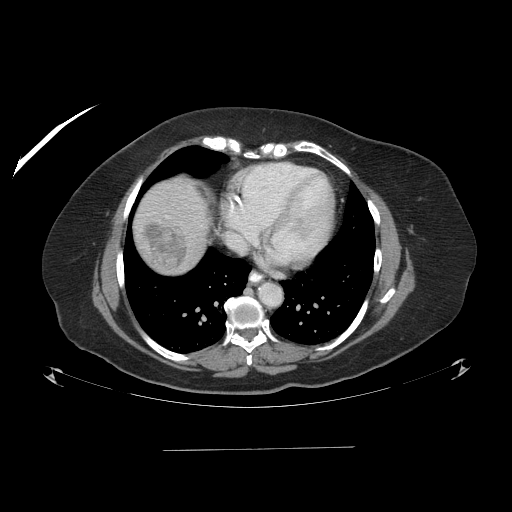
Contrast-enhanced abdominal CT (liver protocol), one axial slice. Slice 83 of 103 in the series (ordered by position). Reconstruction kernel STANDARD. 120 kVp. One of 2 acquisitions stored at this slice position. Soft-tissue window (W 400 / L 40 HU). 2.5 mm slice thickness. 512 × 512 image matrix, field of view 500 × 500 mm. From the clinical record (not read from this slice): diagnosis: hepatocellular carcinoma (patient treated with transarterial chemoembolisation; whether this scan precedes or follows treatment is not stated here); TNM stage (as recorded): Stage-IIIA; Child-Pugh class: A; tumour differentiation: poorly differentiated; tumour nodularity: multinodular.
Outlined on this slice (semi-automatic segmentation, software-assisted and operator-edited):
- liver parenchyma outside the tumour (the mass and vessels are separate outlines, so this box may not span the whole liver): bounding box <134,176,208,272> (left, top, right, bottom; pixels)
- mass: <141,223,187,267>